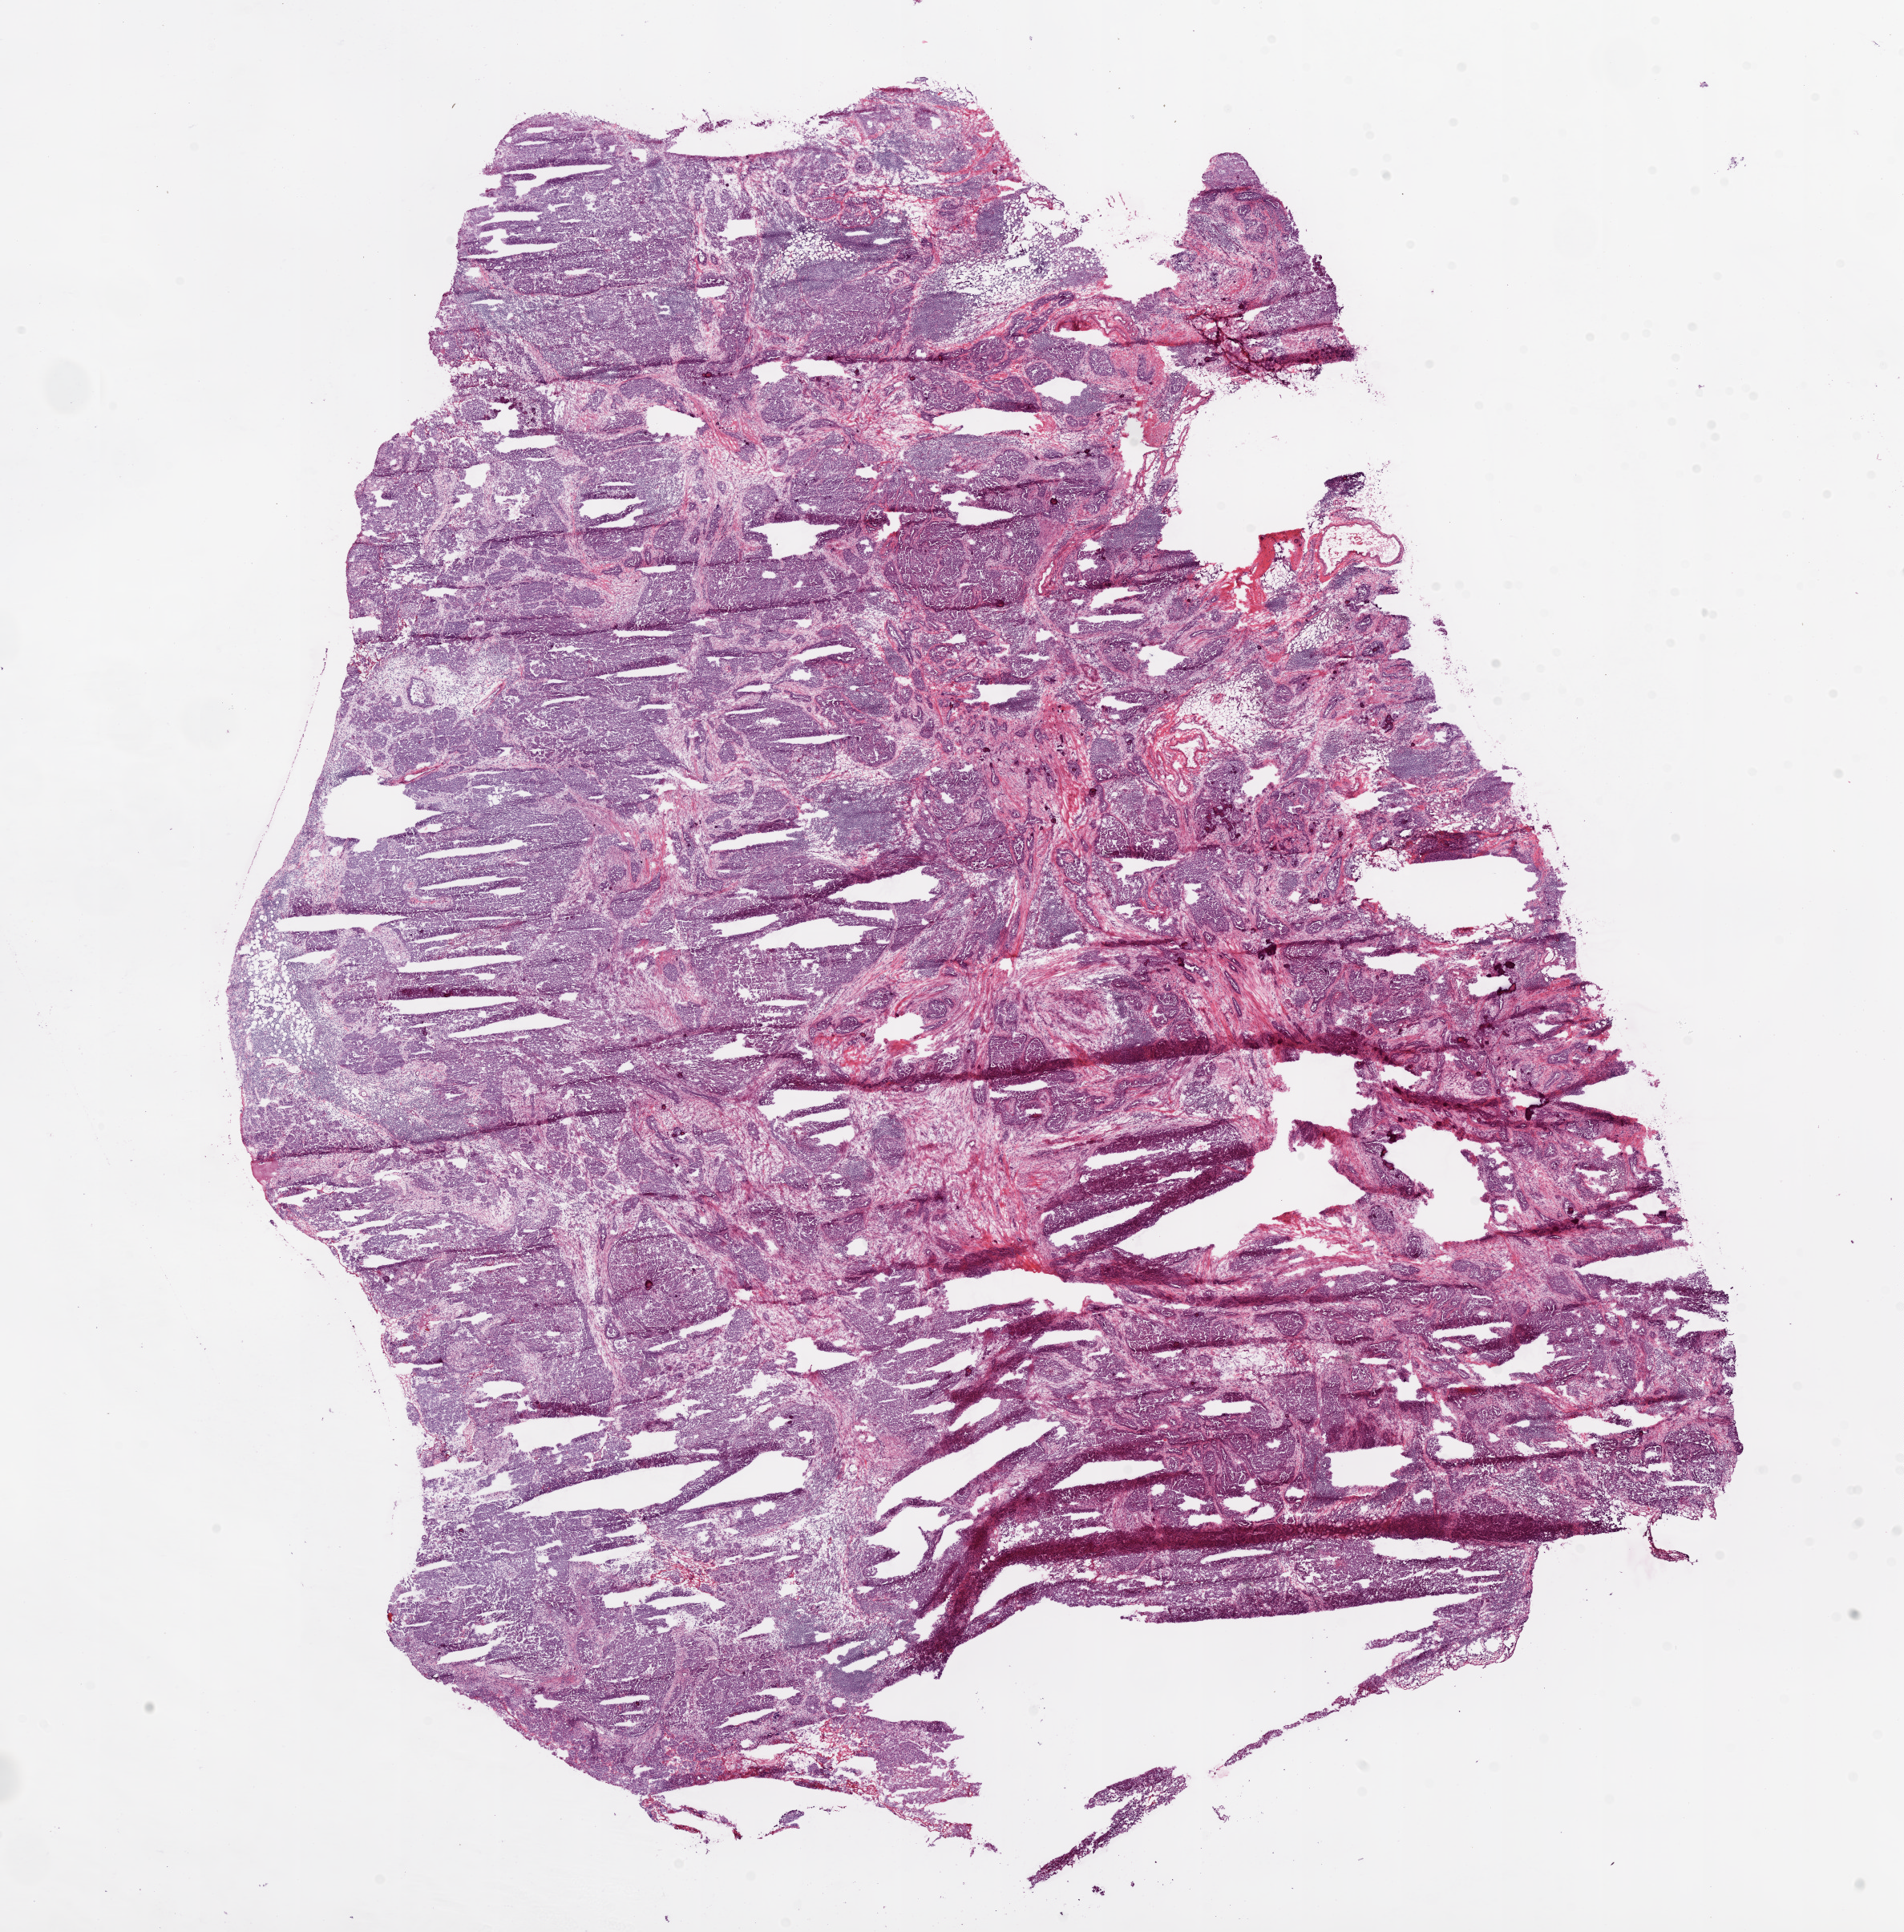
Whole-slide histology image, Hematoxylin and eosin (H&E) stained — a low-resolution overview of the entire scanned area, about 19.1 x 19.3 mm. Frozen section. Ovary, primary tumour sample. Patient: female, age at initial diagnosis 61 years. Histologic grade: G3 (poorly differentiated). Slide review estimates, as recorded: tumour cells 85%, tumour nuclei 94%, normal cells 0%, stromal cells 15%, necrosis 0%.
Diagnosis: Serous cystadenocarcinoma, NOS. FIGO stage: IIIC.